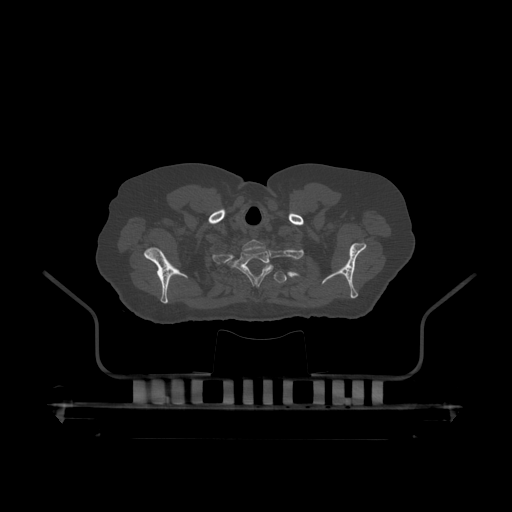
CT including the spine, one axial slice; slice 389 of 390 in the series (ordered by position); reconstruction kernel STANDARD; bone window (W 1800 / L 400 HU); 1.25 mm slice thickness; 512 × 512 image matrix, field of view 650 × 650 mm. Male patient, age 60 years. Case-level facts recorded for this patient, not image findings: primary cancer: prostate.
Outlined on this slice (semi-automatic segmentation, software-assisted and operator-edited):
- T1 vertebra: bounding box (x1, y1, x2, y2) in pixels: (235, 240, 274, 286)
- T2 vertebra: (264, 267, 287, 284)